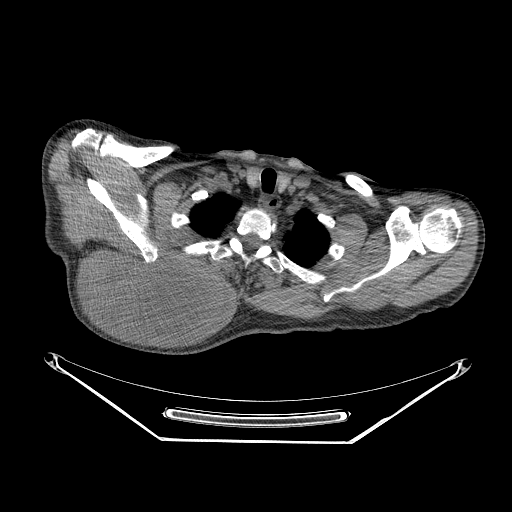
CT of an extremity soft-tissue mass (from a PET/CT study), one axial slice; slice 204 of 267 in the series (ordered by position); reconstruction kernel STANDARD; 140 kVp; soft-tissue window (W 400 / L 40 HU); 3.75 mm slice thickness; 512 × 512 image matrix, field of view 500 × 500 mm. Male patient. From the clinical record (not read from this slice): histological type: pleiomorphic spindle cell undifferentiated; grade: high; site of the primary tumour: right parascapusular.
Outlined on this slice (expert contour drawn on MRI and transferred to this co-registered scan by the dataset authors):
- gross tumour volume including surrounding oedema: box from (x=82, y=244) to (x=236, y=332) px
- gross tumour volume (mass): (x=82, y=247)–(x=222, y=328)